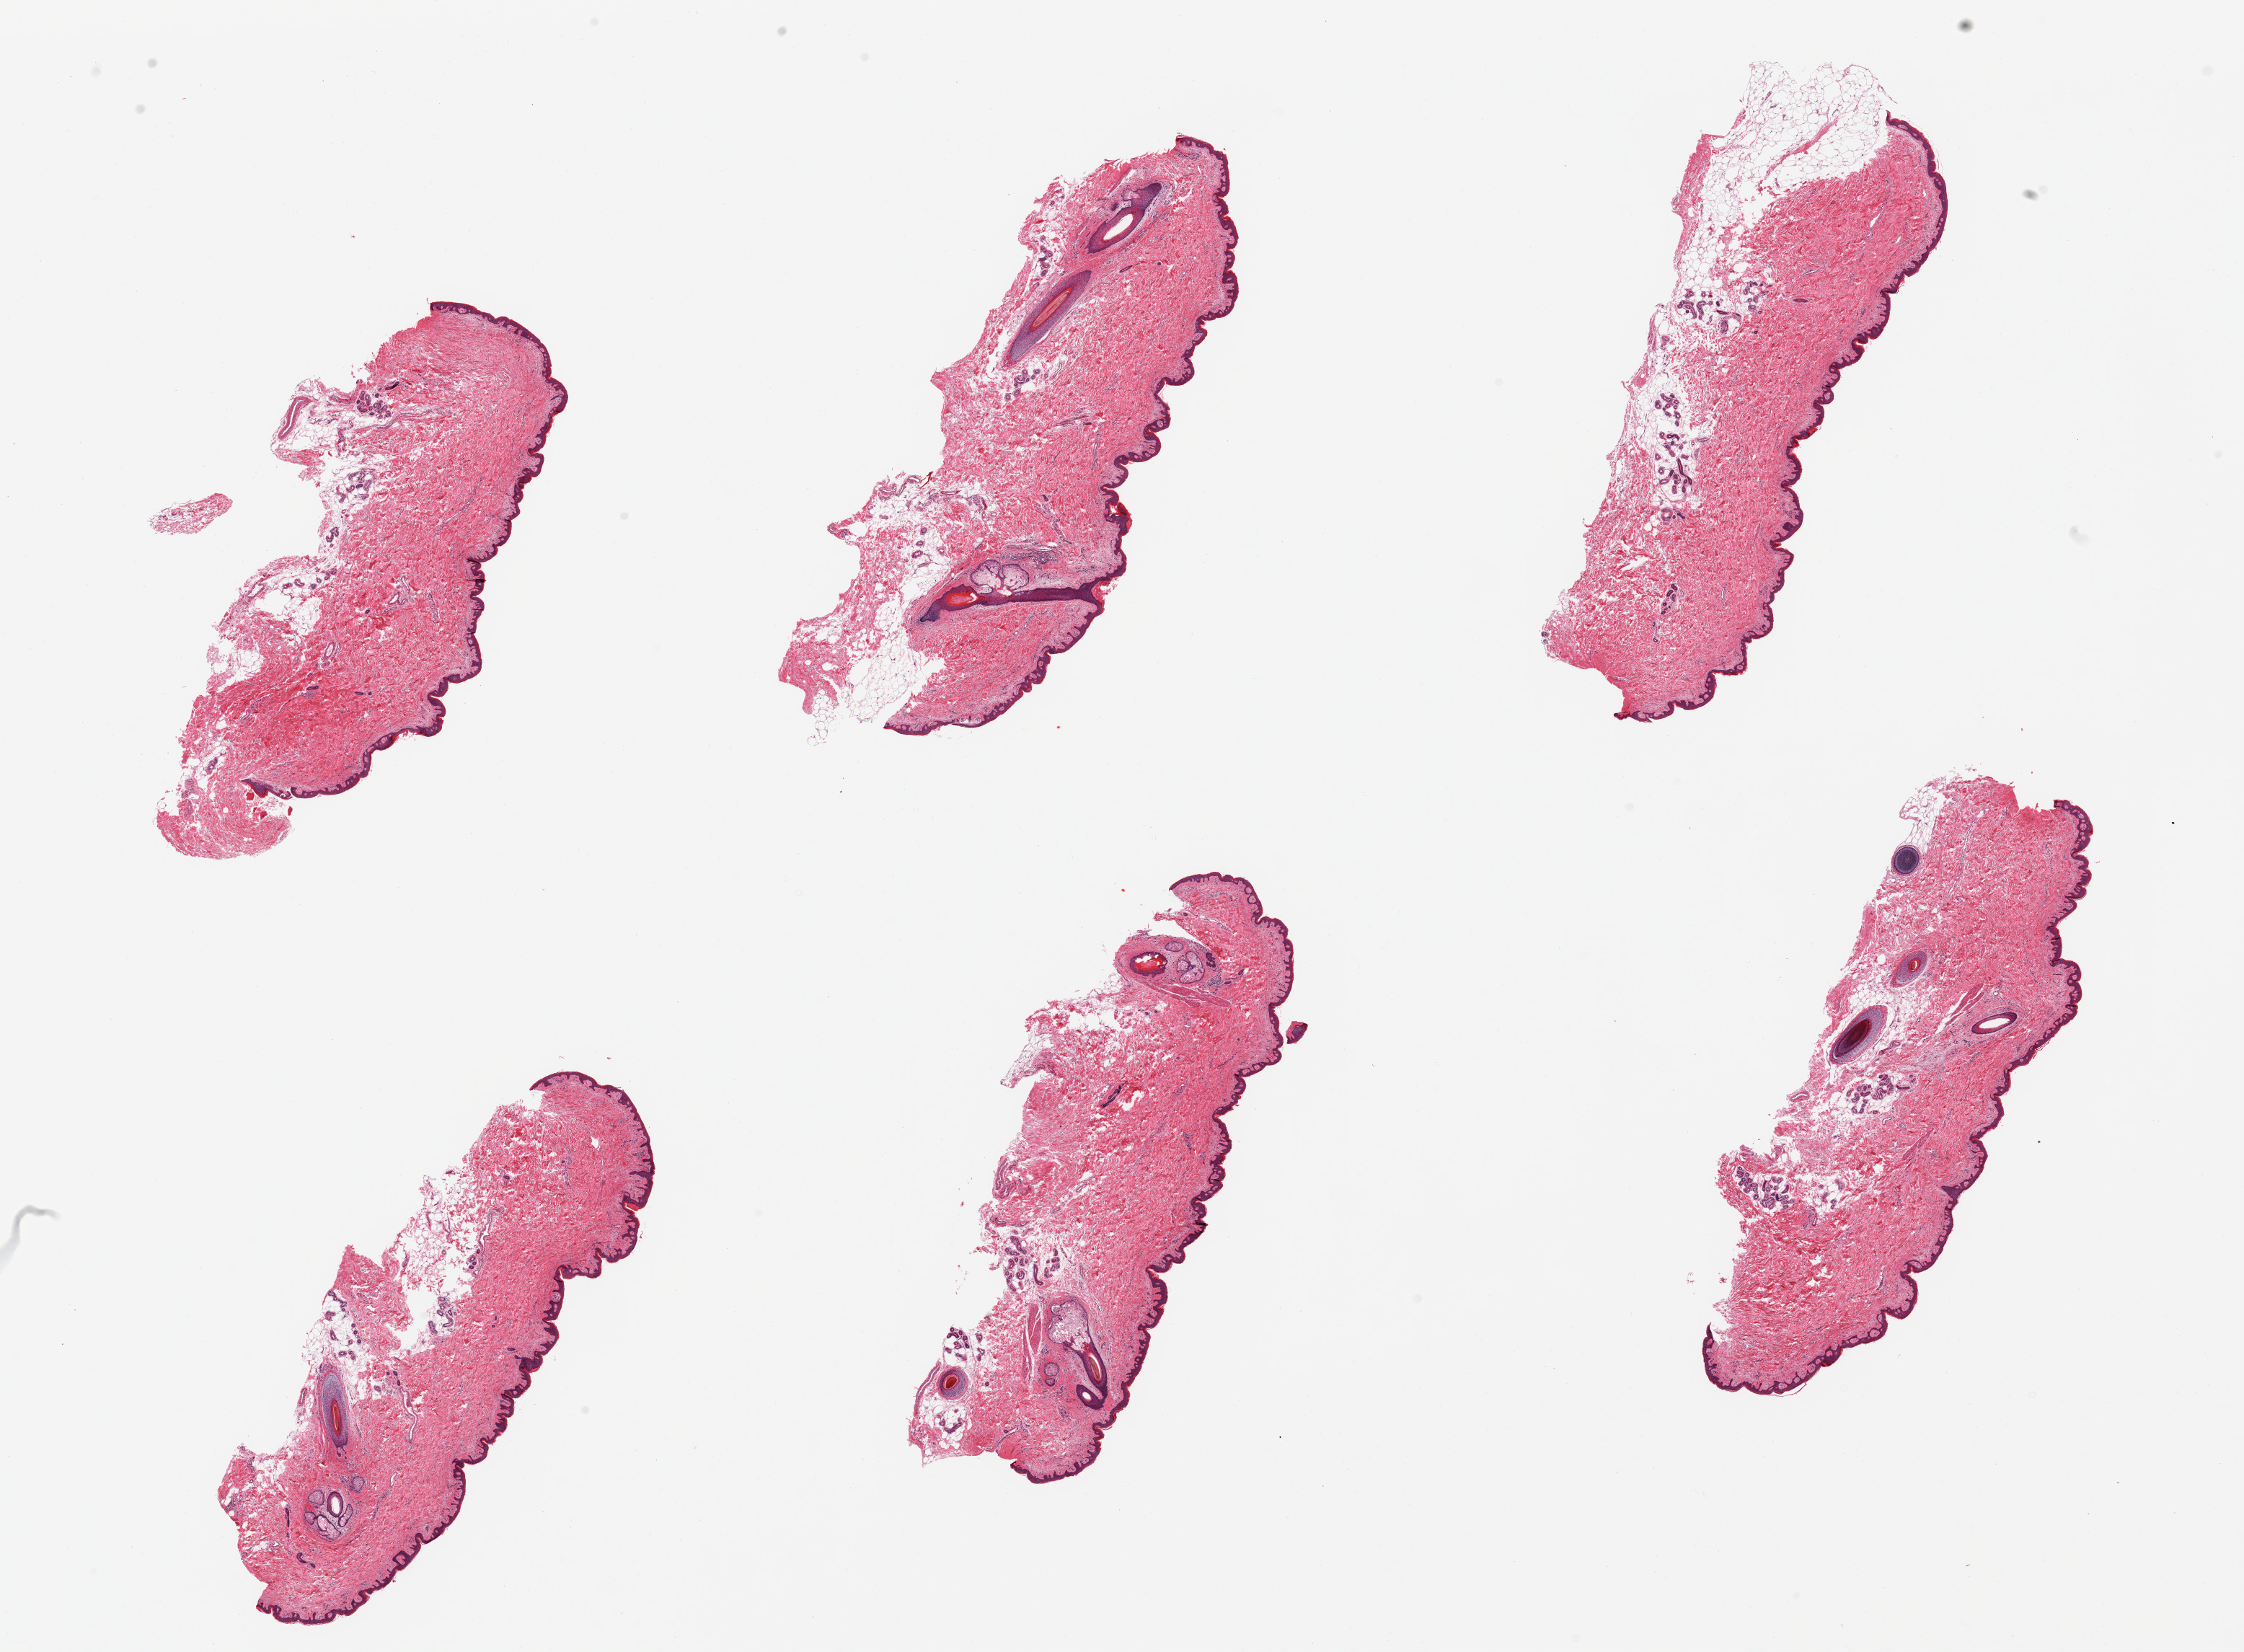
H&E whole-slide image, whole scanned area (about 24.6 x 18.1 mm, acquisition: 20x scan) shown as a low-resolution overview, PAXgene-fixed paraffin-embedded (PFPE) section, target tissue: skin of suprapubic region, donor tissue sample. Male donor.
Pathologist's review note for this sample: 6 pieces, minimal adherent fat, squamous epithelium is ~50-60 microns.